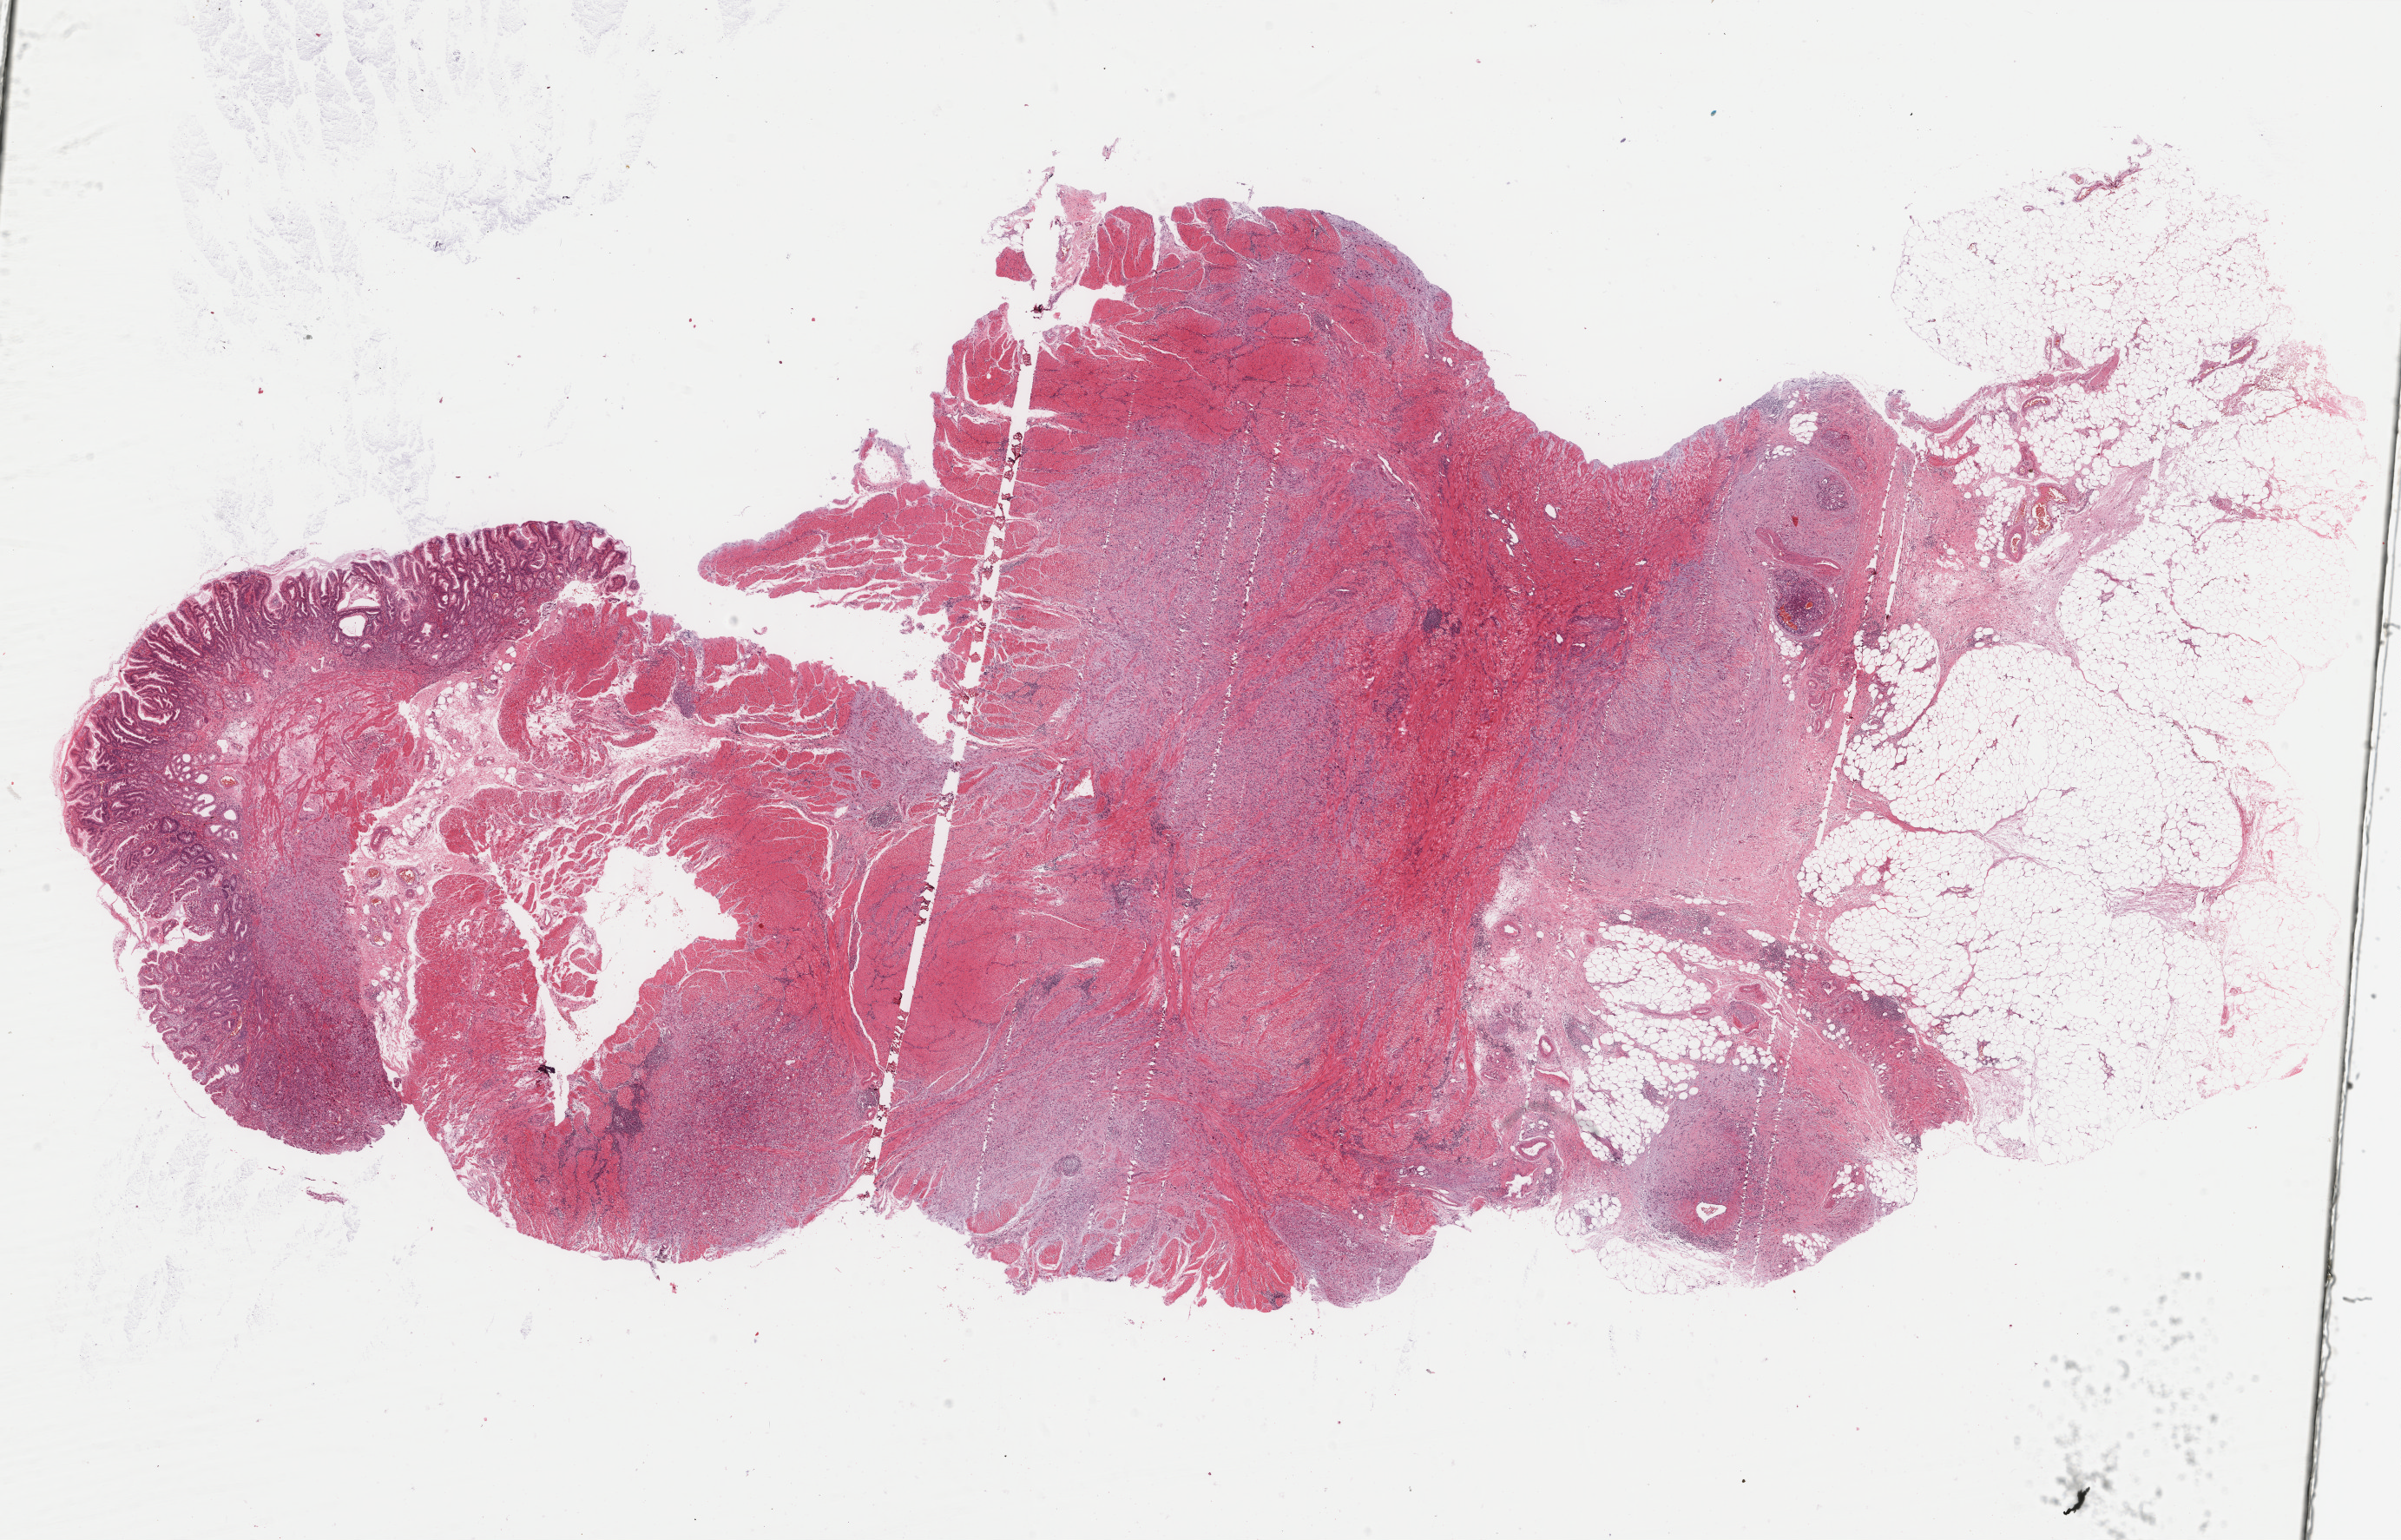
Hematoxylin and eosin (H&E) stained whole-slide image, a low-resolution overview of the entire scanned area, about 22.0 x 14.1 mm (slide scanned at 40x), formalin-fixed paraffin-embedded (FFPE) diagnostic section, stomach, primary tumour sample. Patient: male, age at initial diagnosis 58 years. Histologic grade: G3 (poorly differentiated).
Histologic diagnosis: Carcinoma, diffuse type (gastric antrum). AJCC pathologic stage: IIA (7th edition).